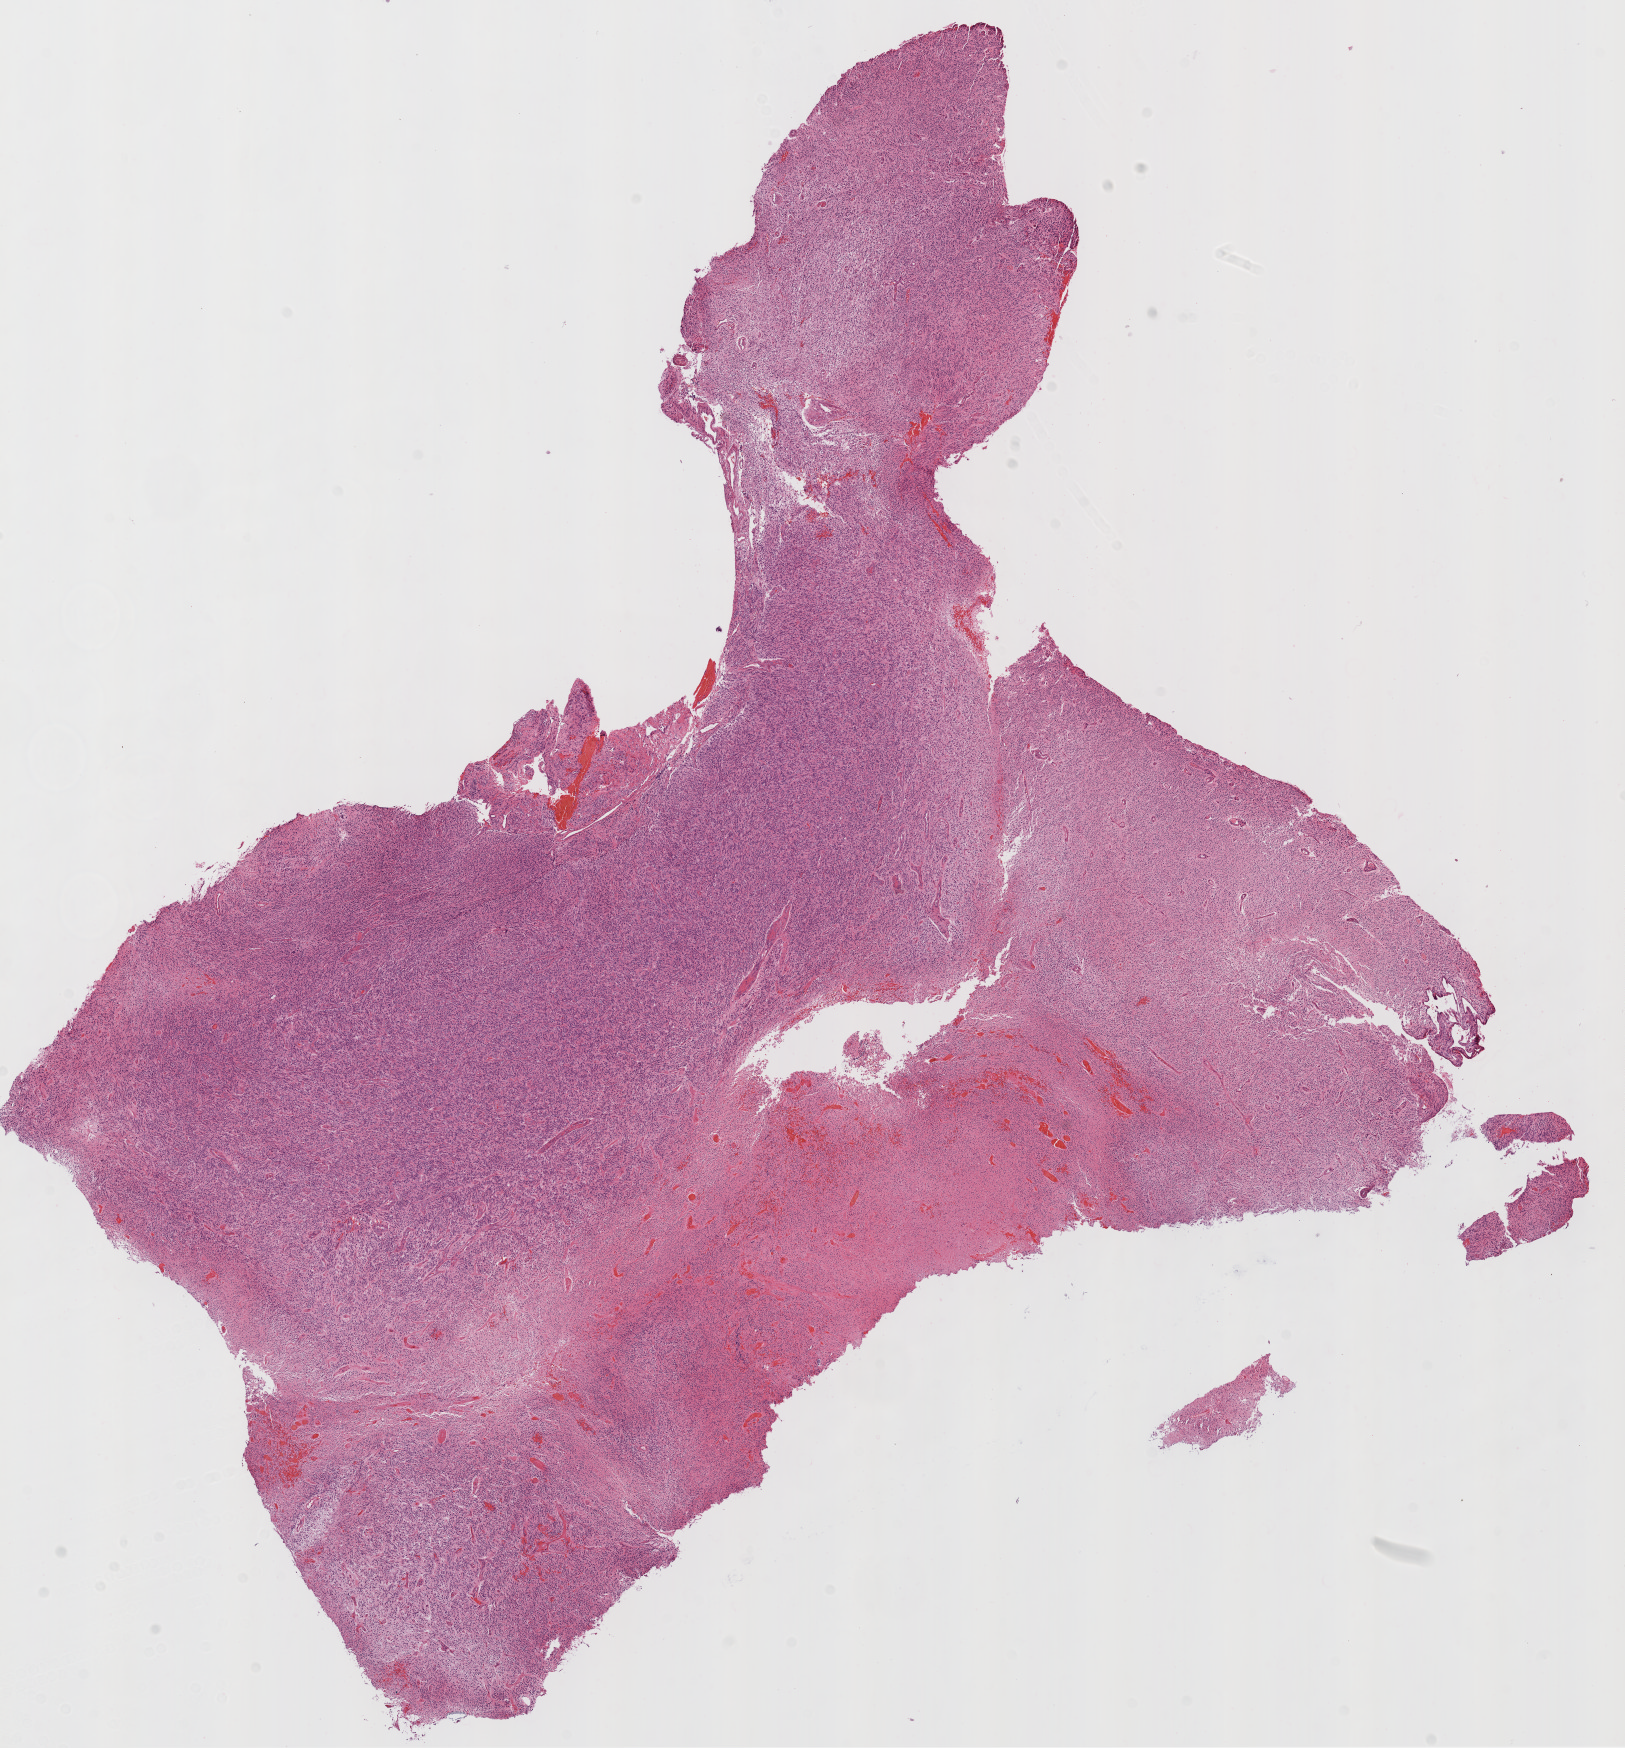
Hematoxylin and eosin (H&E) stained whole-slide image, a low-resolution overview of the entire scanned area, about 13.0 x 14.0 mm (acquisition: 20x scan), formalin-fixed paraffin-embedded (FFPE) diagnostic section, brain, primary tumour sample. Male, age 76 years at initial diagnosis.
Diagnosis: Glioblastoma.